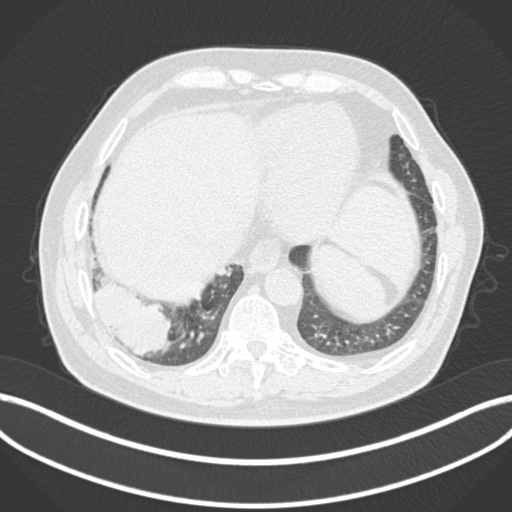
Chest CT, one axial slice; slice 26 of 200 in the series (ordered by position); lung window (W 1500 / L -600 HU); 1 mm slice thickness; 512 × 512 image matrix, field of view 400 × 400 mm. Patient: male, 59 years.
Structures marked on this image (bounding box drawn by a radiologist):
- lung tumour (recorded histology: adenocarcinoma): bounding box <85,271,172,358> (left, top, right, bottom; pixels)